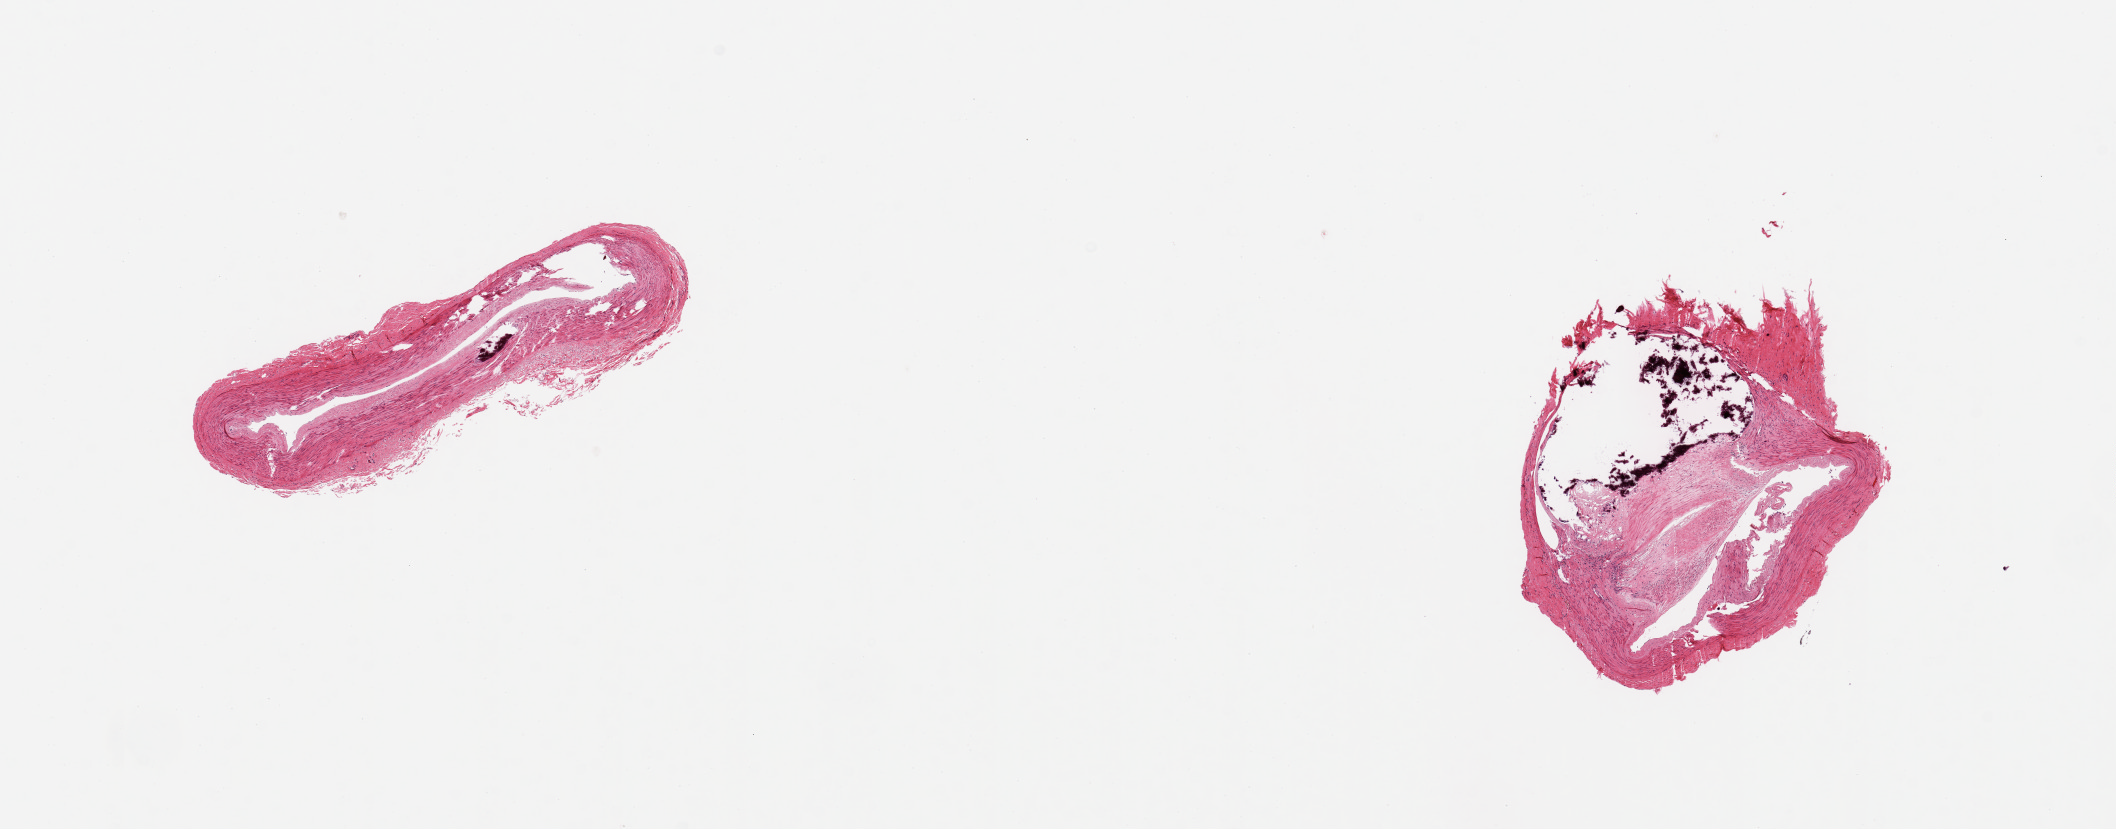
Digitized hematoxylin and eosin (H&E)-stained section, whole scanned area (about 16.7 x 6.6 mm, slide scanned at 20x) shown as a low-resolution overview. PAXgene-fixed paraffin-embedded (PFPE) section. Section of tibial artery (target tissue). Tissue donor sample. Donor: male.
Pathologist's review note for this sample: 2 pieces; one include focus of medial calcification and mild plaque, second shows significant calcific atherosclerosis with profound luminal narrowing.